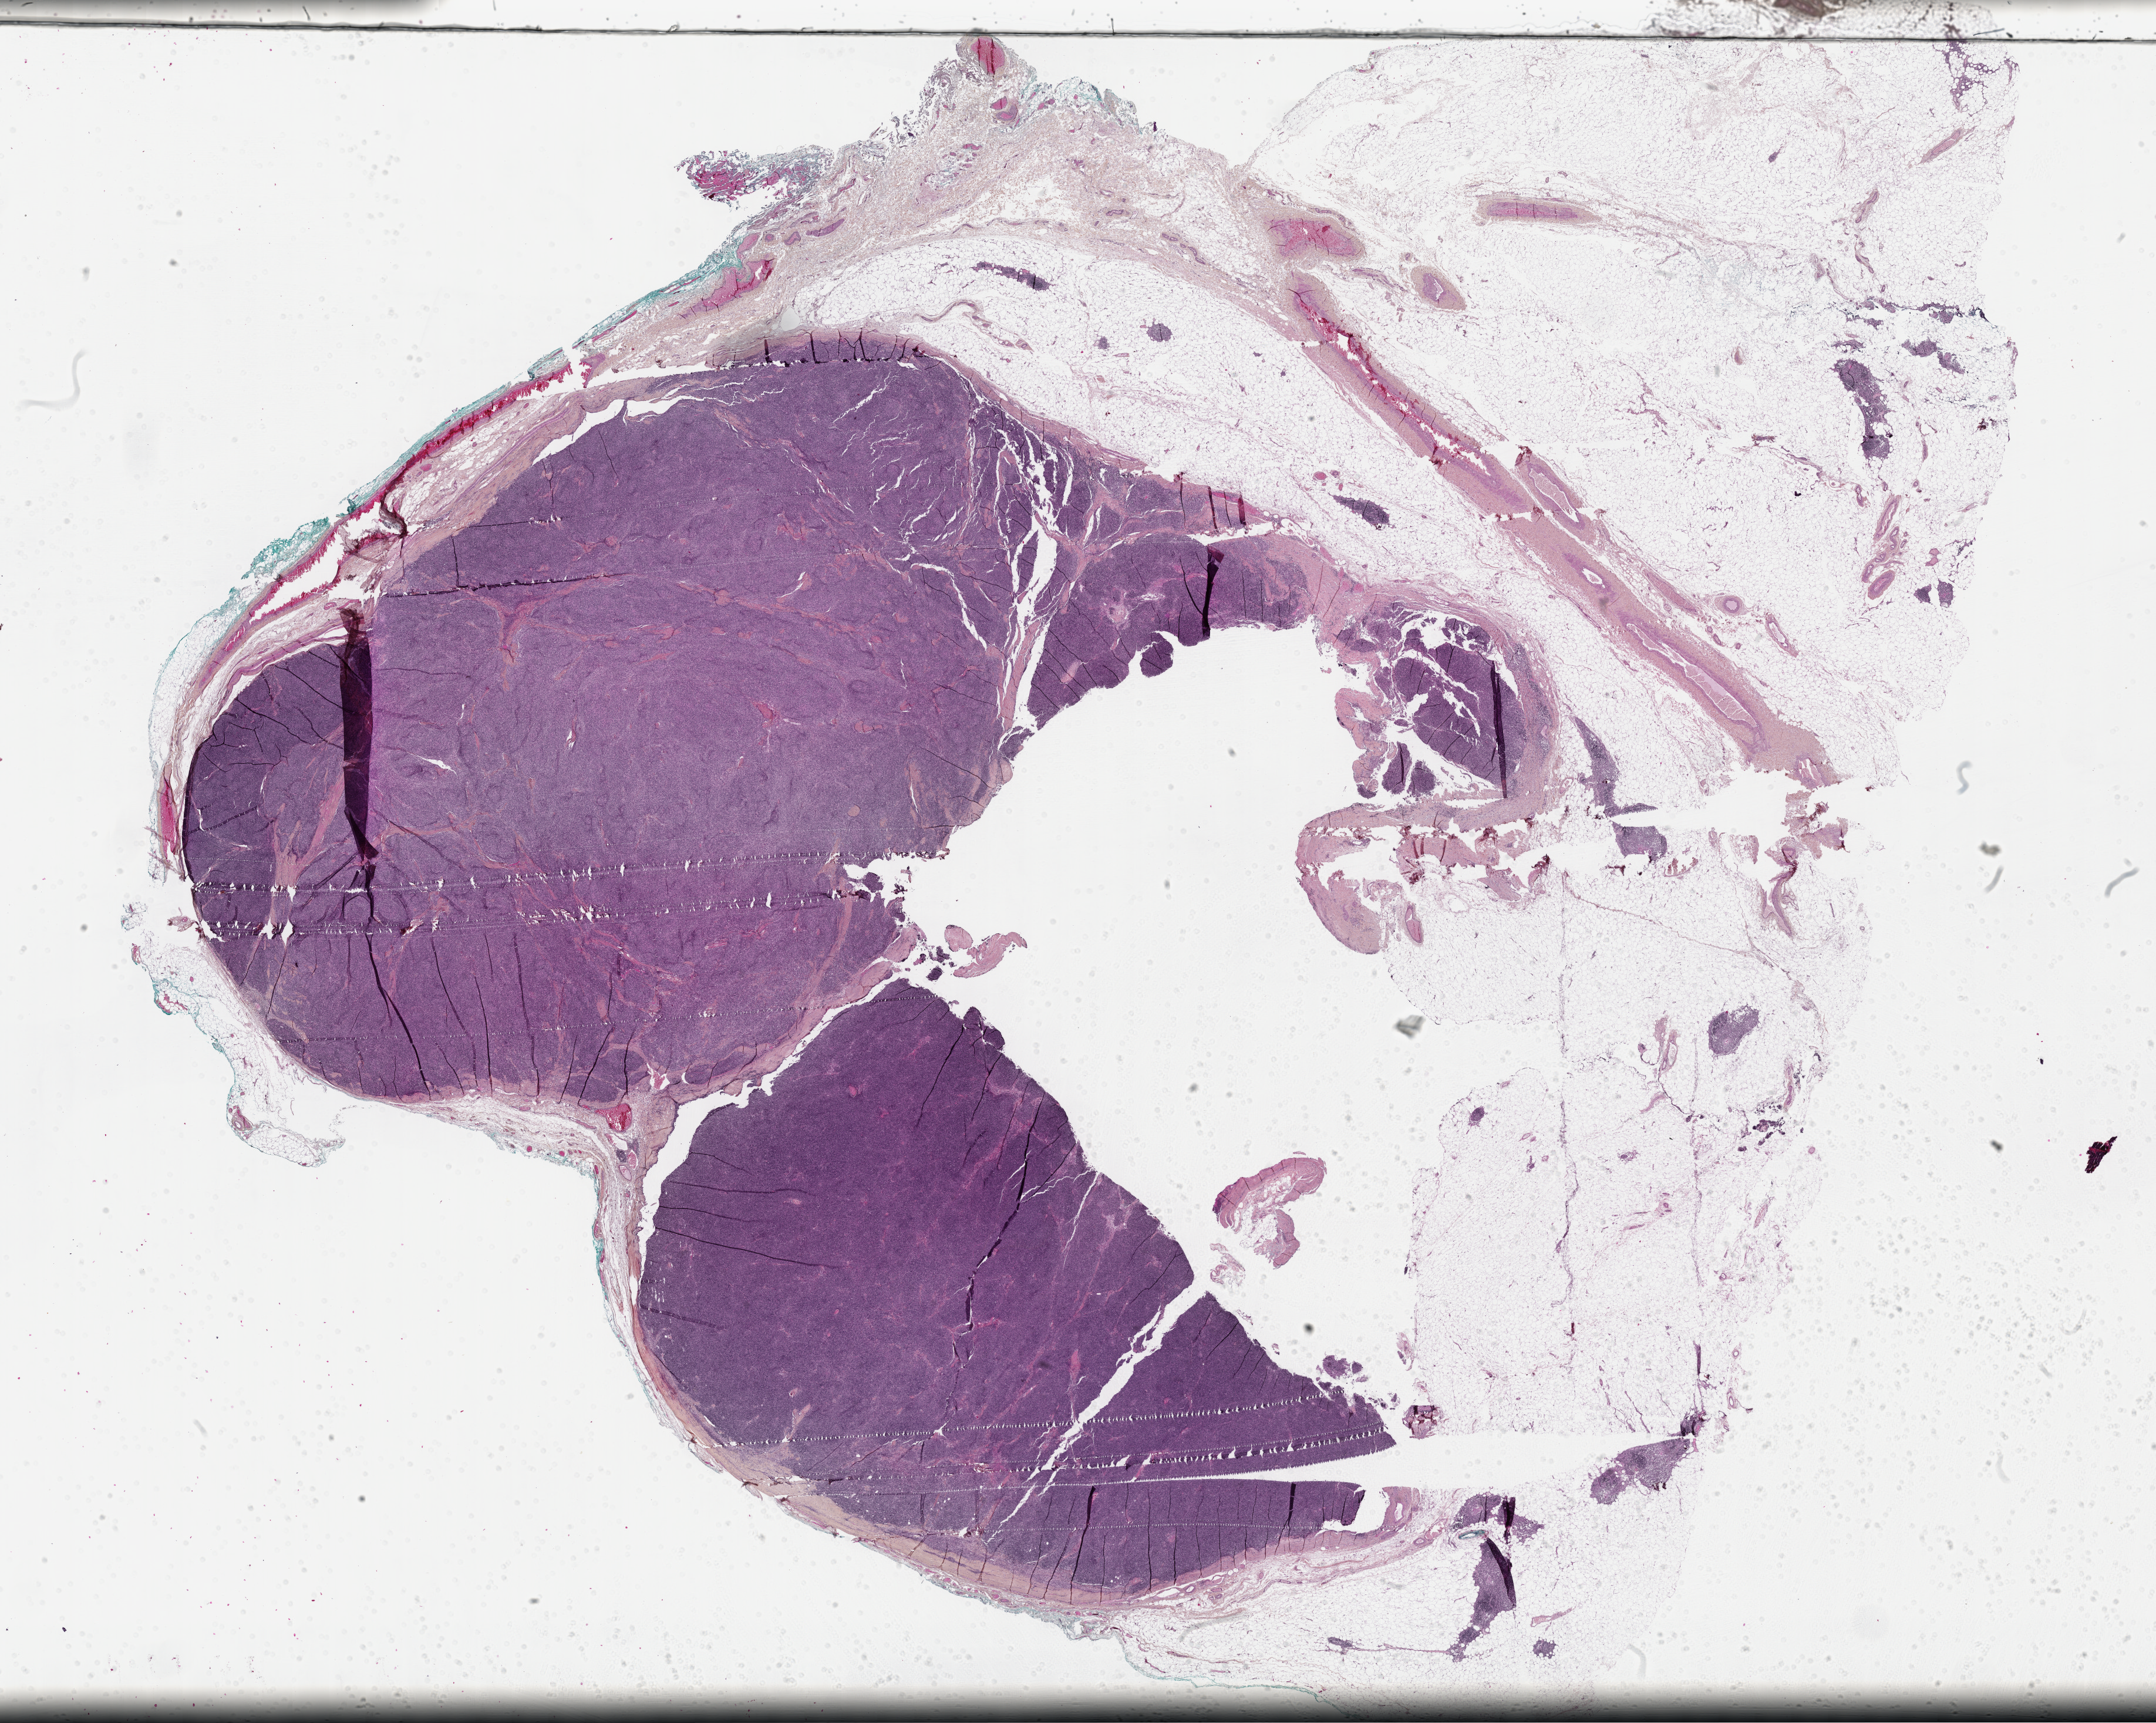
Whole-slide histology image, H&E-stained, low-resolution overview of the scanned area, about 29.7 x 23.7 mm (acquisition: 40x scan), formalin-fixed paraffin-embedded (FFPE) diagnostic section, primary tumour sample from the thymus. Female patient; age at initial diagnosis 76 years.
Histologic diagnosis: Thymoma, type AB, malignant.